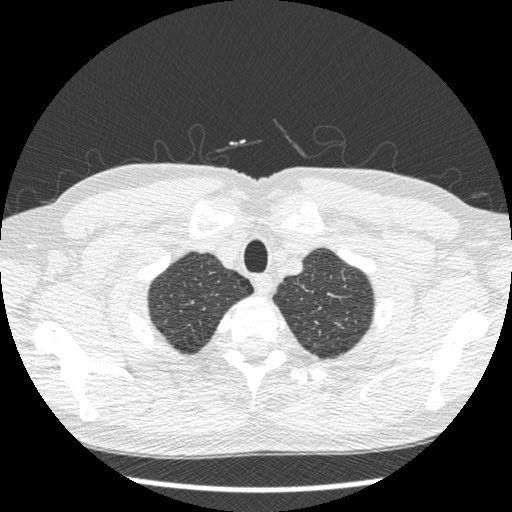
Low-dose screening chest CT, one axial slice. Slice 404 of 439 in the series (ordered by position). Lung window (W 1500 / L -600 HU). 1.25 mm slice thickness. 512 × 512 image matrix.
Outlined on this slice (outlined manually by an expert reader):
- lesion 1 (nodule, upper lobe of left lung): bounding box (x1, y1, x2, y2) in pixels: (335, 323, 344, 329)